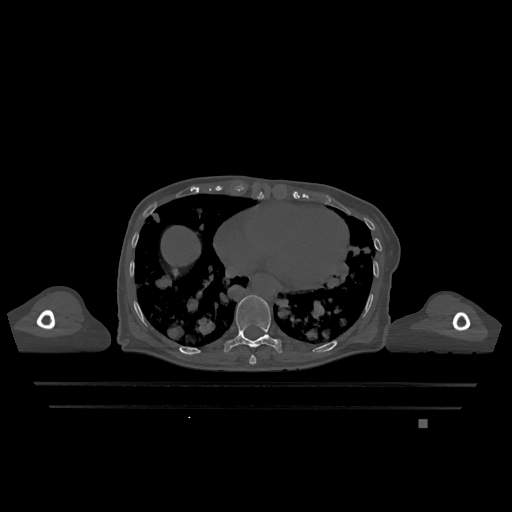
CT including the spine, one axial slice. Position 645 of 1317 along the scan axis. Bone window (W 1800 / L 400 HU). 0.5 mm slice thickness. 512 × 512 image matrix, field of view 500 × 500 mm. Patient: female, 74 years. Case-level facts recorded for this patient, not image findings: primary cancer: lung.
Annotated regions visible in this slice (semi-automatically segmented with operator editing):
- T10 vertebra: box from (x=223, y=295) to (x=283, y=353) px
- T9 vertebra: (x=249, y=355)–(x=257, y=365)